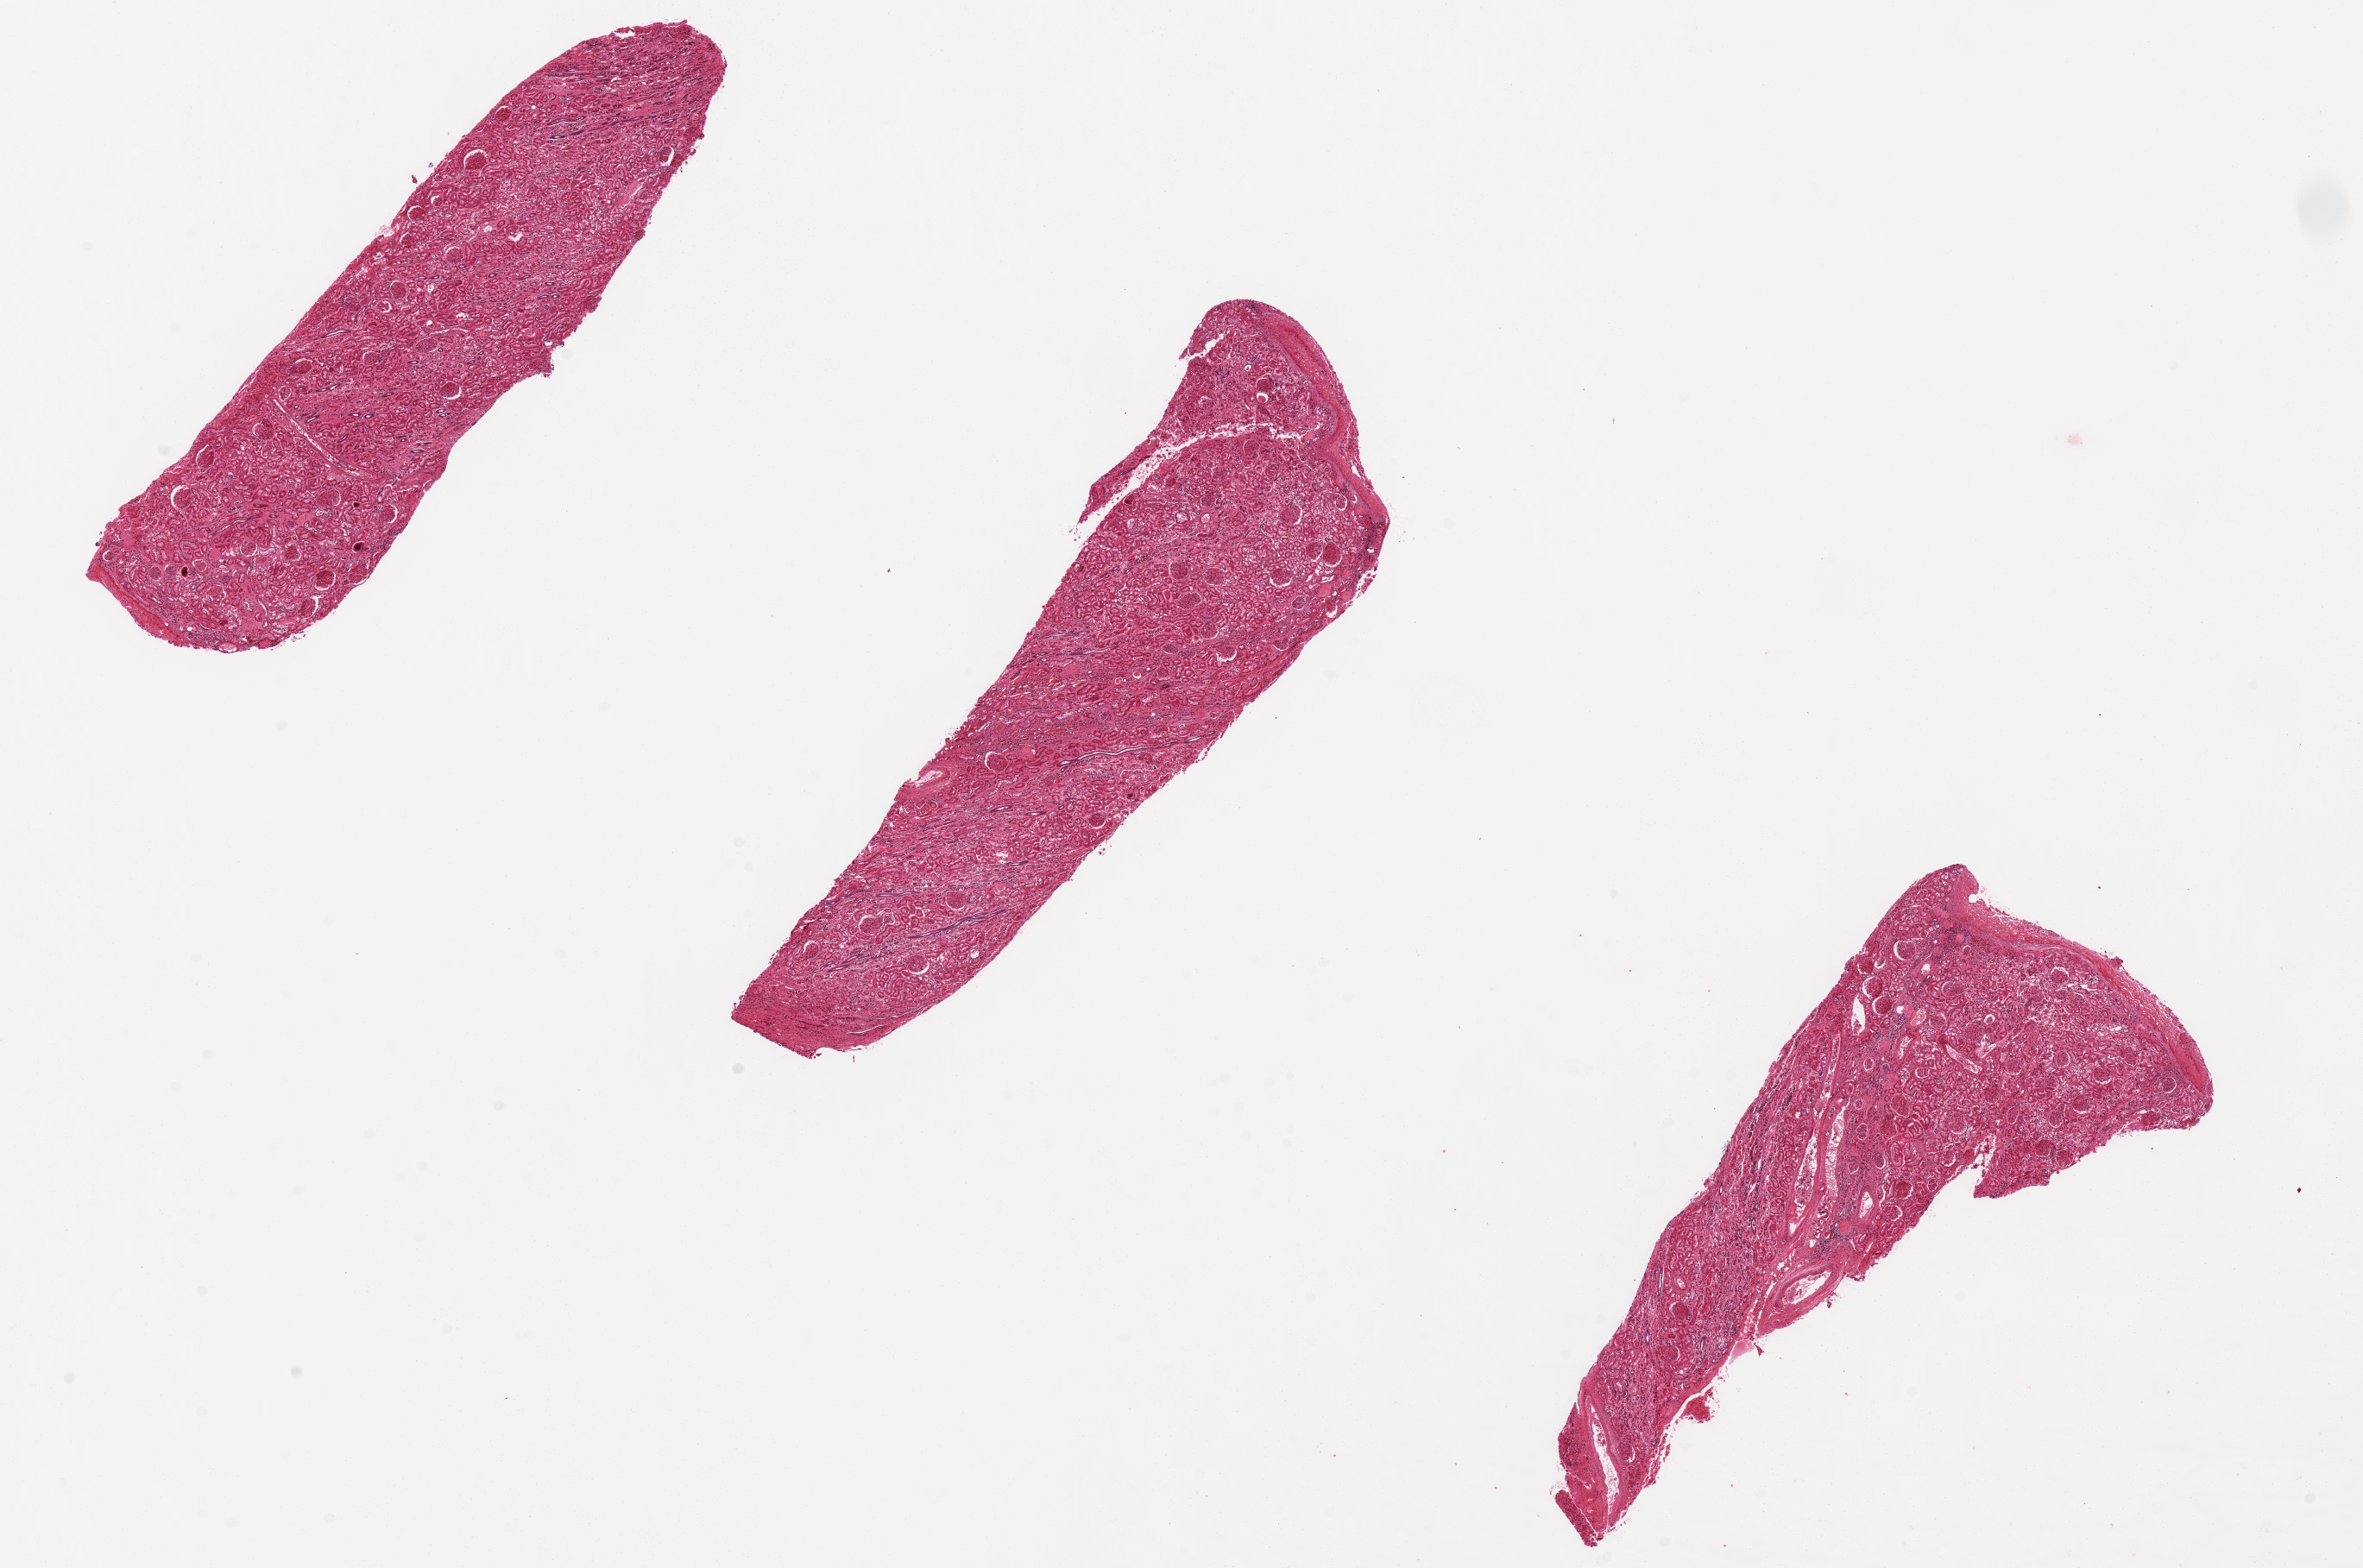
Whole-slide image, haematoxylin and eosin stain, a low-resolution overview of the entire scanned area, about 21.7 x 14.4 mm (slide scanned at 20x), PAXgene-fixed paraffin-embedded (PFPE) section, target tissue: renal cortex, donor tissue sample. Donor sex: male.
Reviewer comment on this tissue sample: 3 pieces 7.5x1.8mm.